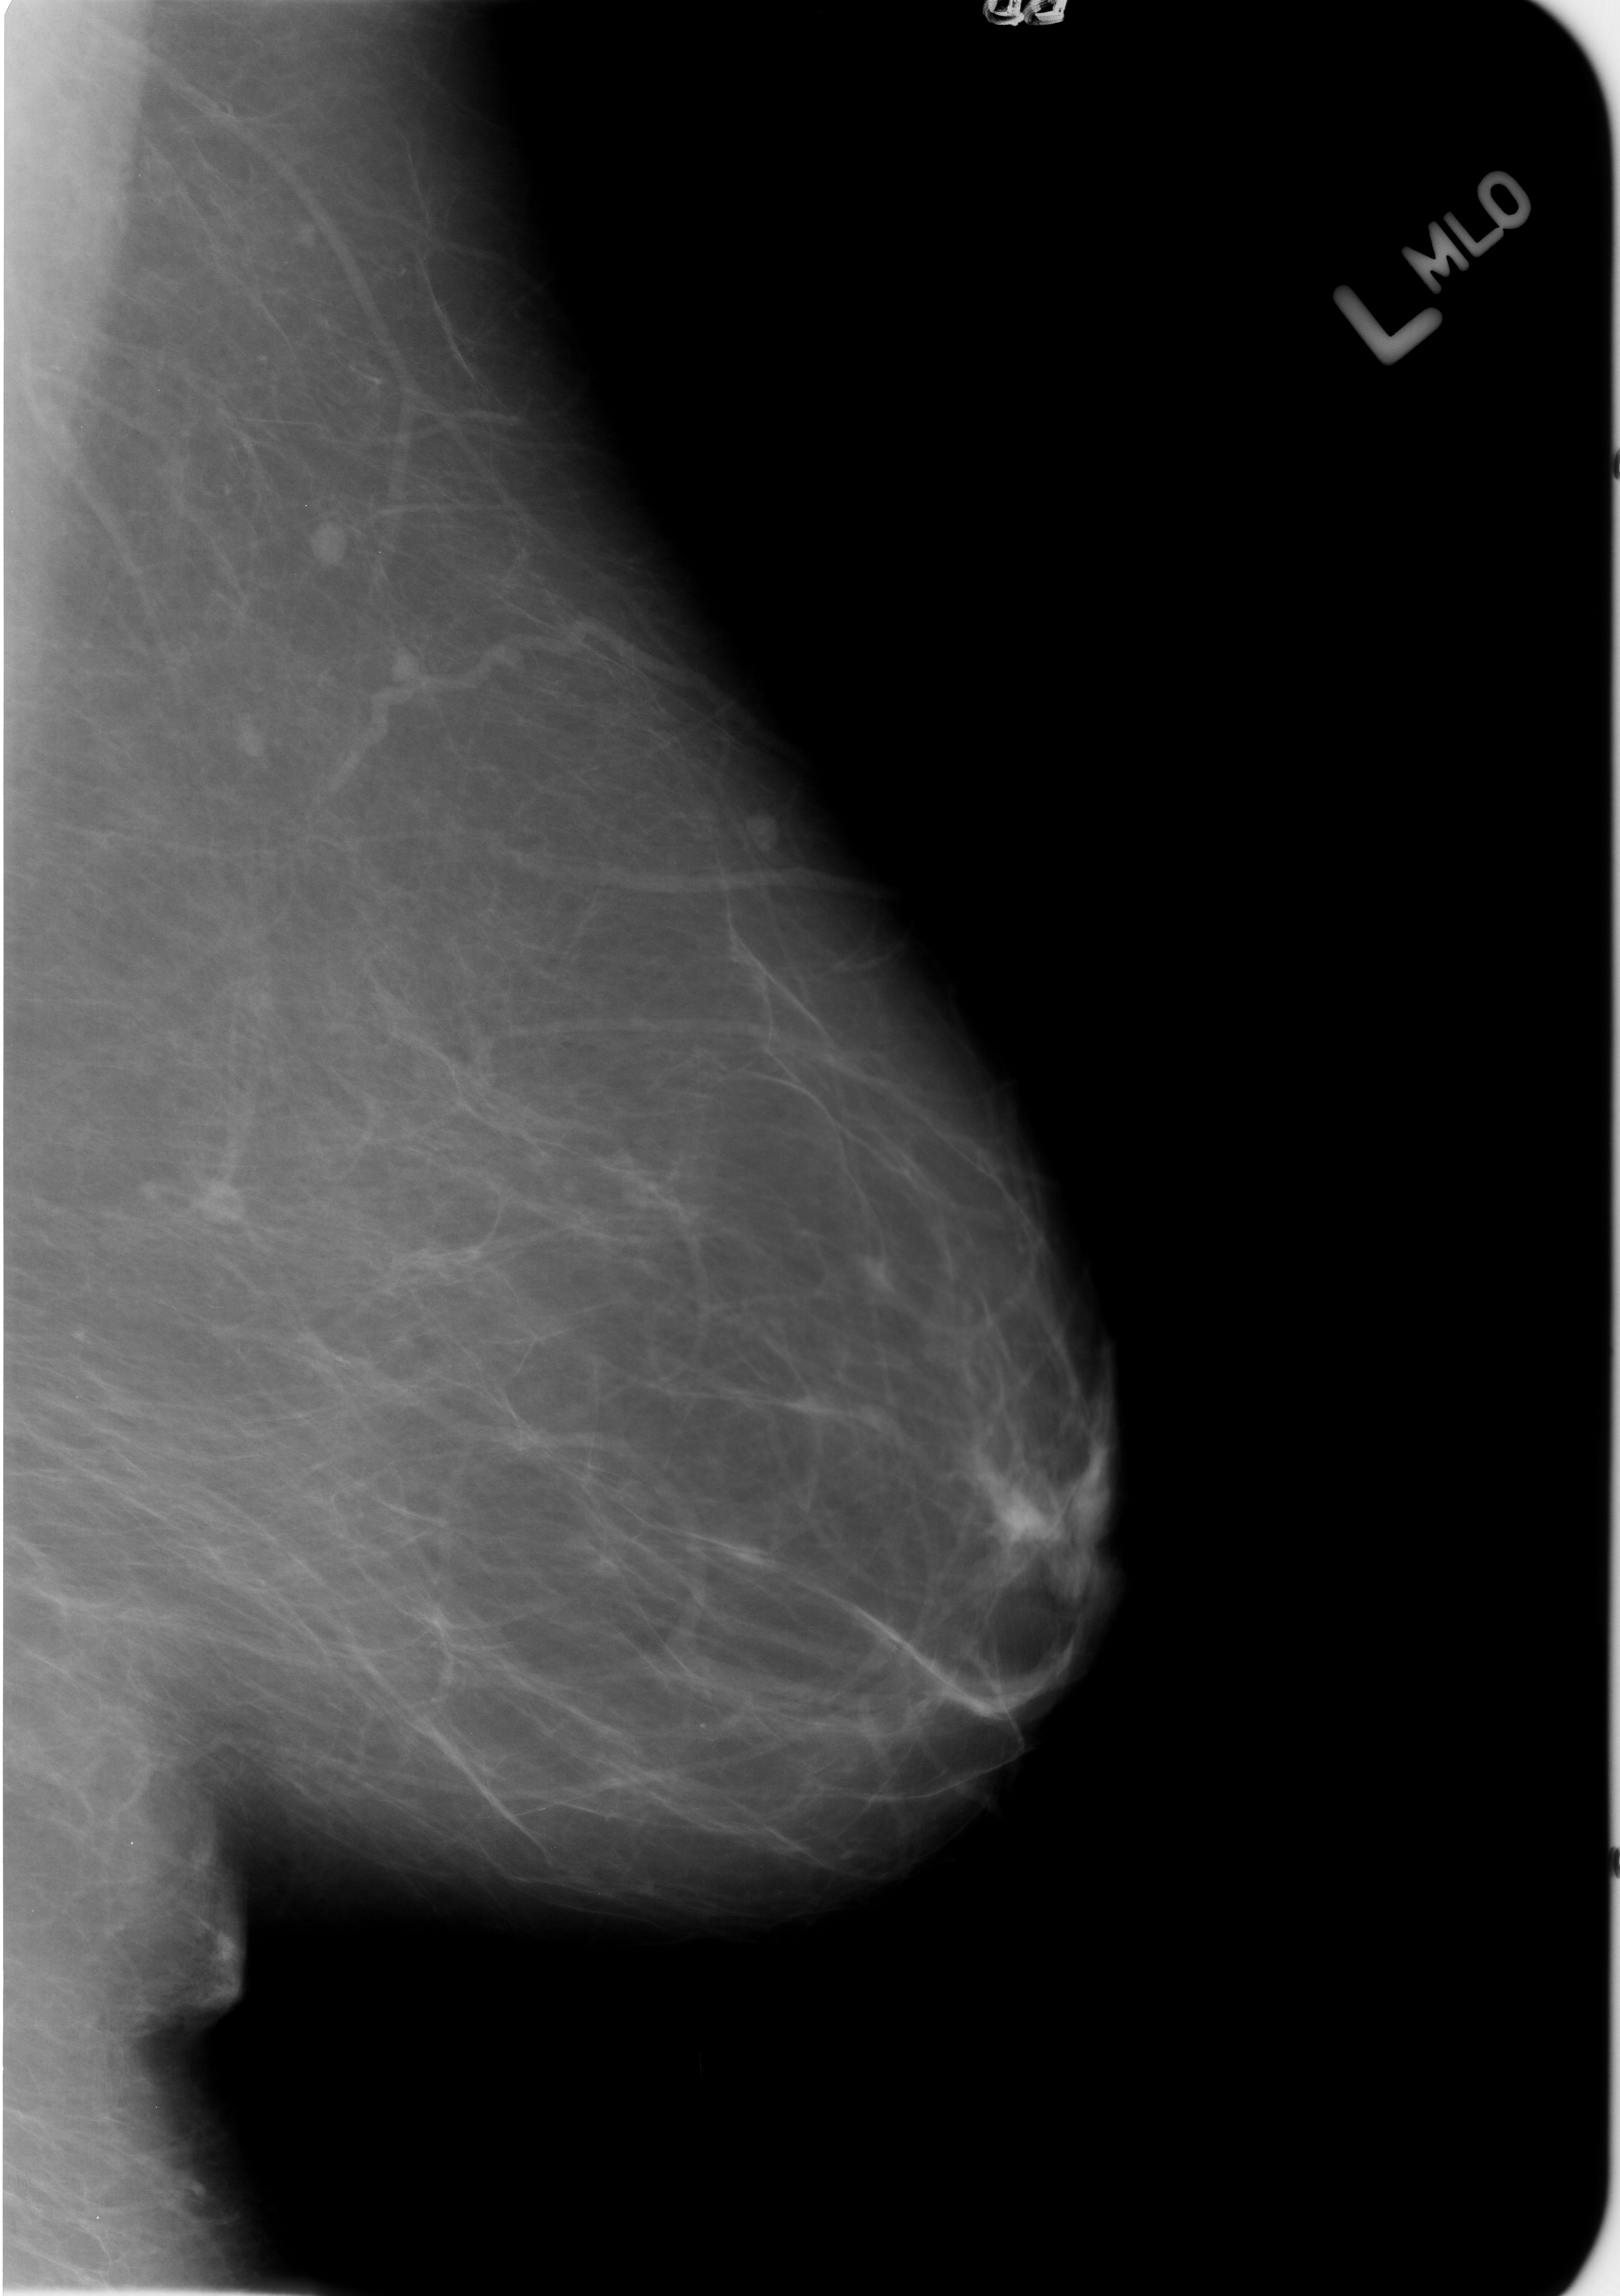
Scanned film-screen mammogram, left breast, MLO view, breast composition: almost entirely fatty (BI-RADS density category 1 of 4).
Radiologist-marked abnormalities on this image: Finding 1 of 5: mass, shape lymph node, margins circumscribed; BI-RADS assessment category 2; subtlety rating 4 on a 1 (subtle) to 5 (obvious) scale; benign; no additional work-up was recommended (benign without callback). Finding 2 of 5: mass, shape lymph node, margins circumscribed; BI-RADS assessment category 2; subtlety rating 4 on a 1 (subtle) to 5 (obvious) scale; benign; no additional work-up was recommended (benign without callback). Finding 3 of 5: mass, shape lymph node, margins circumscribed; BI-RADS assessment category 2; benign; no additional work-up was recommended (benign without callback). Finding 4 of 5: mass, shape lymph node, margins circumscribed; BI-RADS assessment category 2; subtlety rating 4 on a 1 (subtle) to 5 (obvious) scale; benign; no additional work-up was recommended (benign without callback). Finding 5 of 5: mass, shape lymph node, margins circumscribed; BI-RADS assessment category 2; subtlety rating 4 on a 1 (subtle) to 5 (obvious) scale; benign; no additional work-up was recommended (benign without callback).